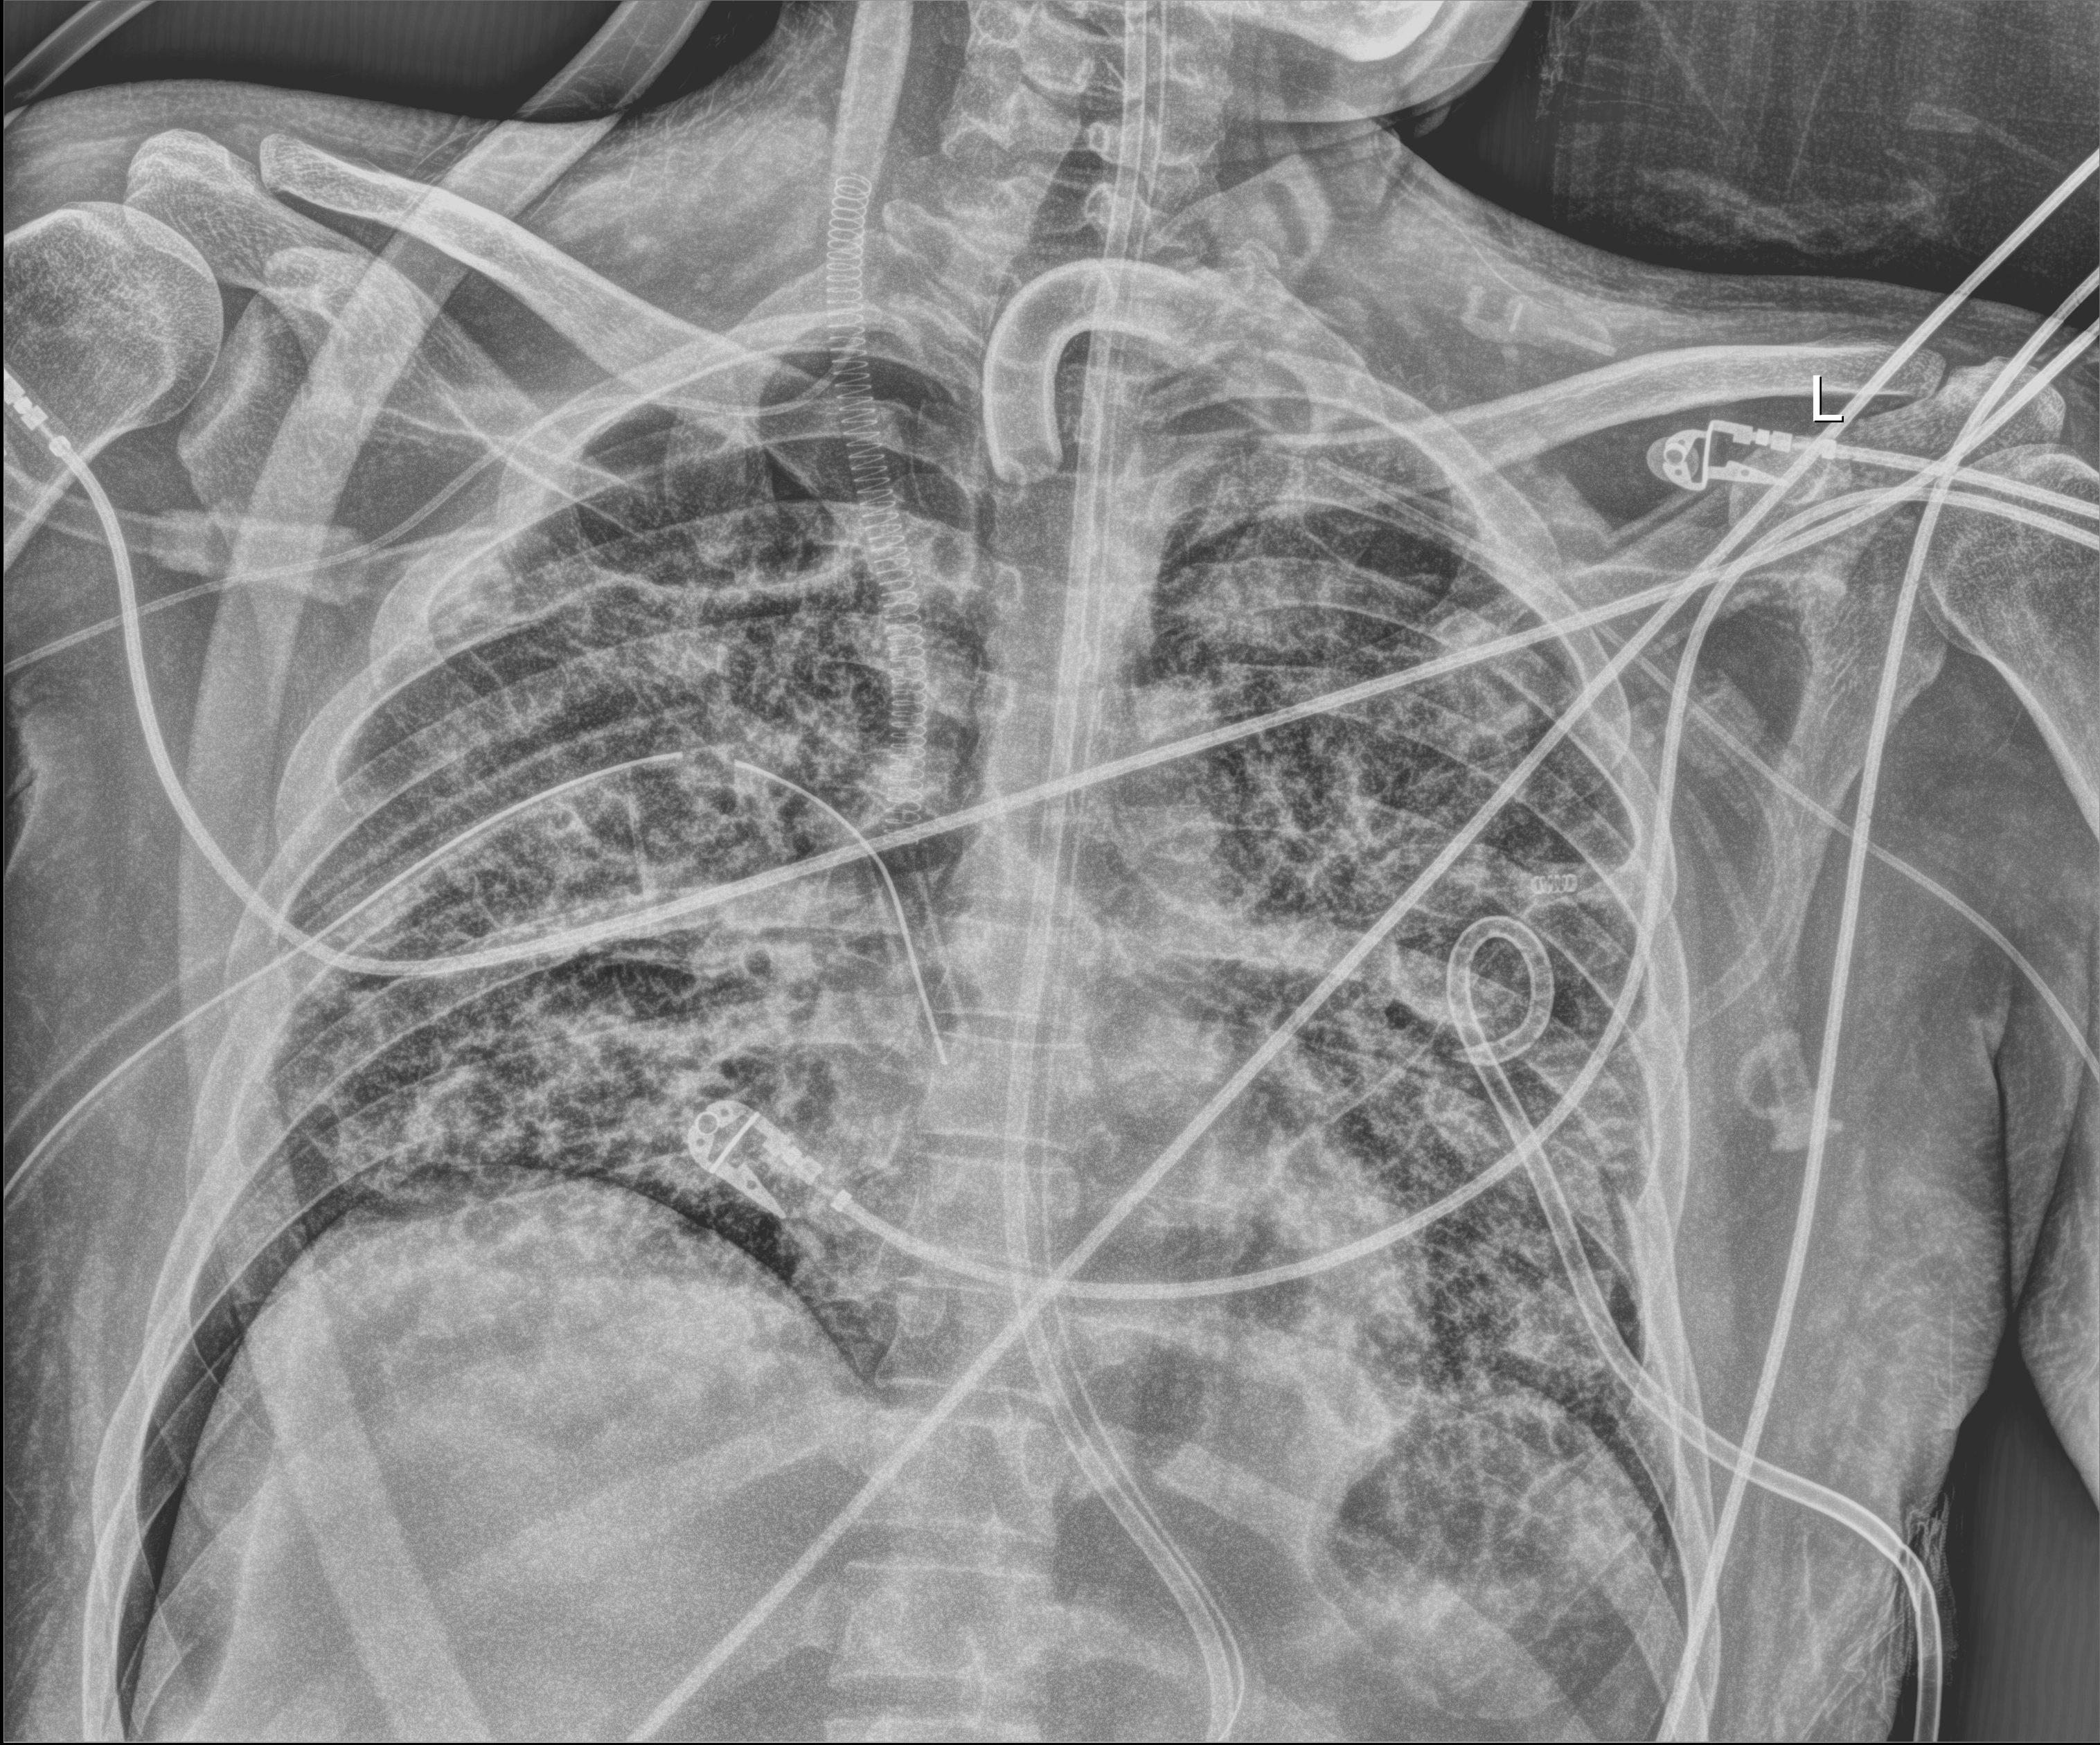
Chest radiograph (digital radiography), anteroposterior (AP) projection. Patient hospitalised with COVID-19, aged 18–59 years.
Hospital-stay facts (about this admission, not read from this image; timing relative to this image not recorded): admitted to intensive care during this hospital stay: yes; diabetes (admission record): no.